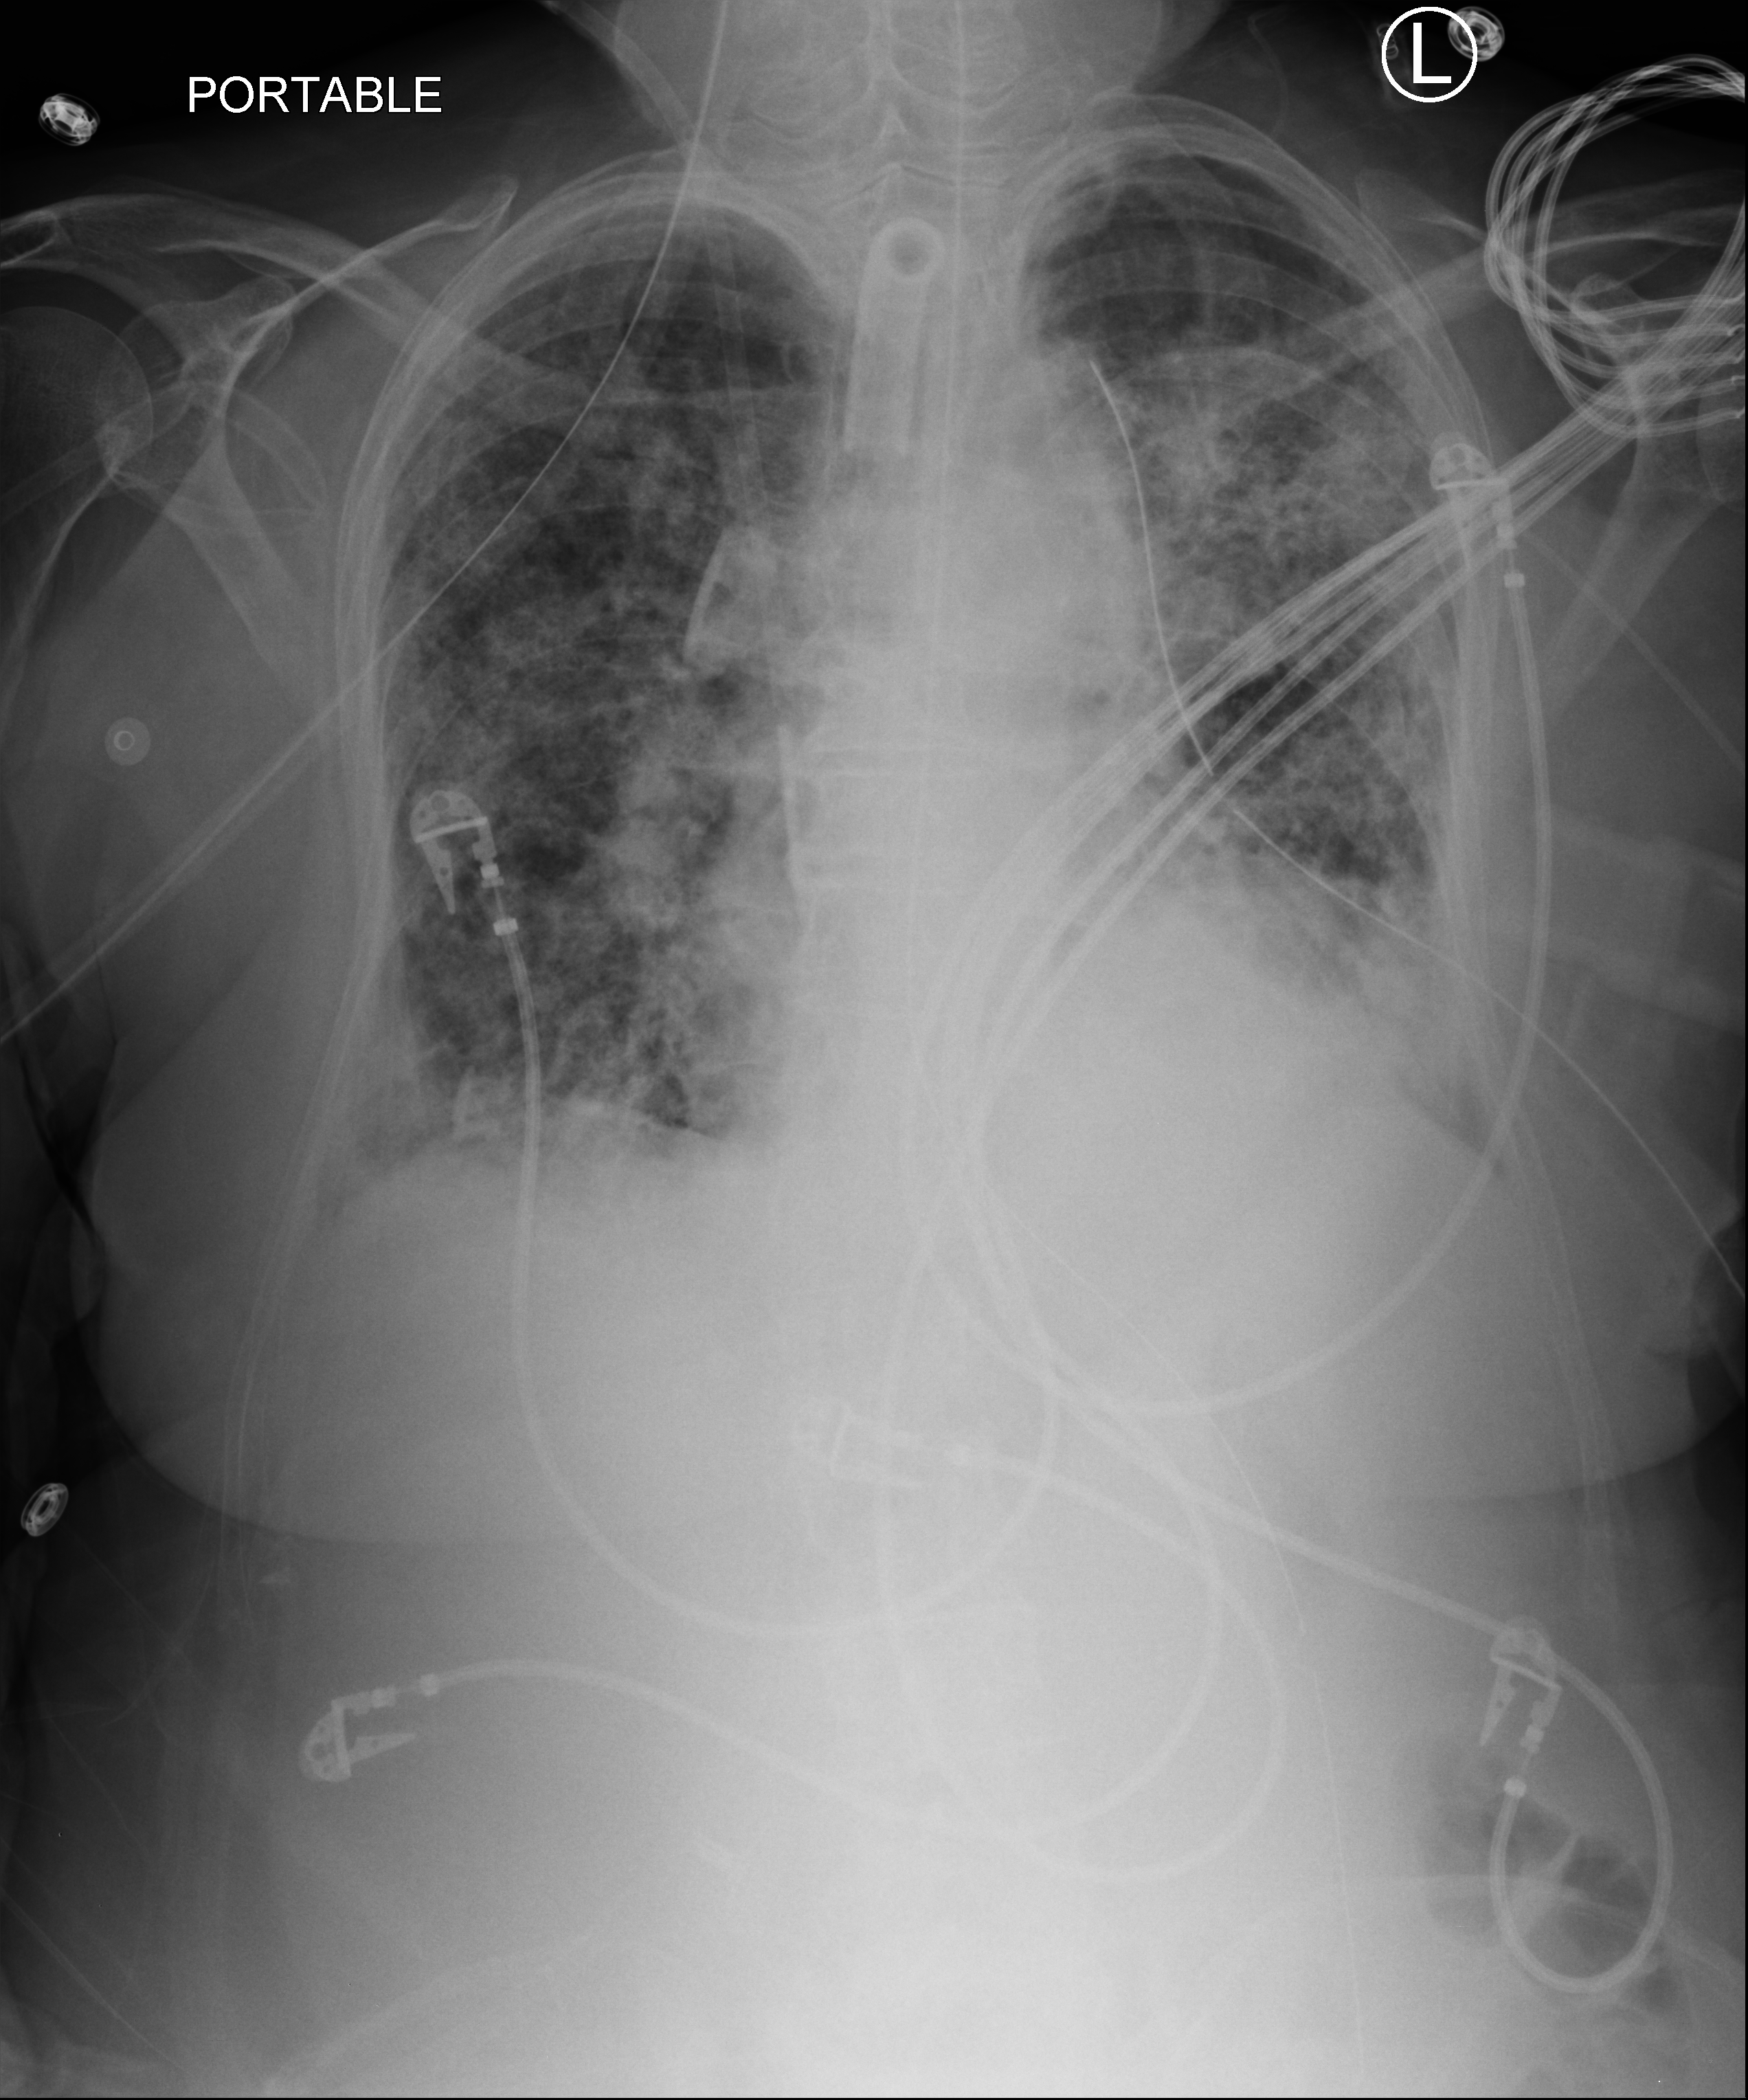
Portable chest radiograph; anteroposterior (AP) projection. Patient hospitalised with COVID-19; female, aged 75–90 years.
Hospital-stay facts (about this admission, not read from this image; timing relative to this image not recorded): admitted to intensive care during this hospital stay: yes; COPD (admission record): no; mechanically ventilated during this hospital stay: yes.